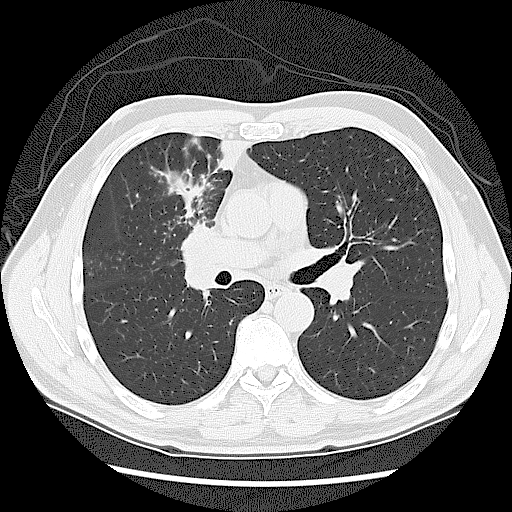
Low-dose screening chest CT, axial slice, baseline annual screen, lung window (W 1500 / L -600 HU), 2.5 mm slice thickness, slice 61 of 131 in the series, 512 × 512 image matrix, field of view 360 × 360 mm. Male participant, aged 60 years at enrolment. Current smoker at enrolment.
• Expert reader's lesion annotation, bounding box [x1, y1, x2, y2] px = [158, 215, 240, 305].
• Screening reader's record for this exam: no non-calcified nodule ≥4 mm recorded.
• Lung cancer was diagnosed 41 days after this screen: small cell carcinoma, NOS, right upper lobe, stage IIIA (AJCC 6th edition).